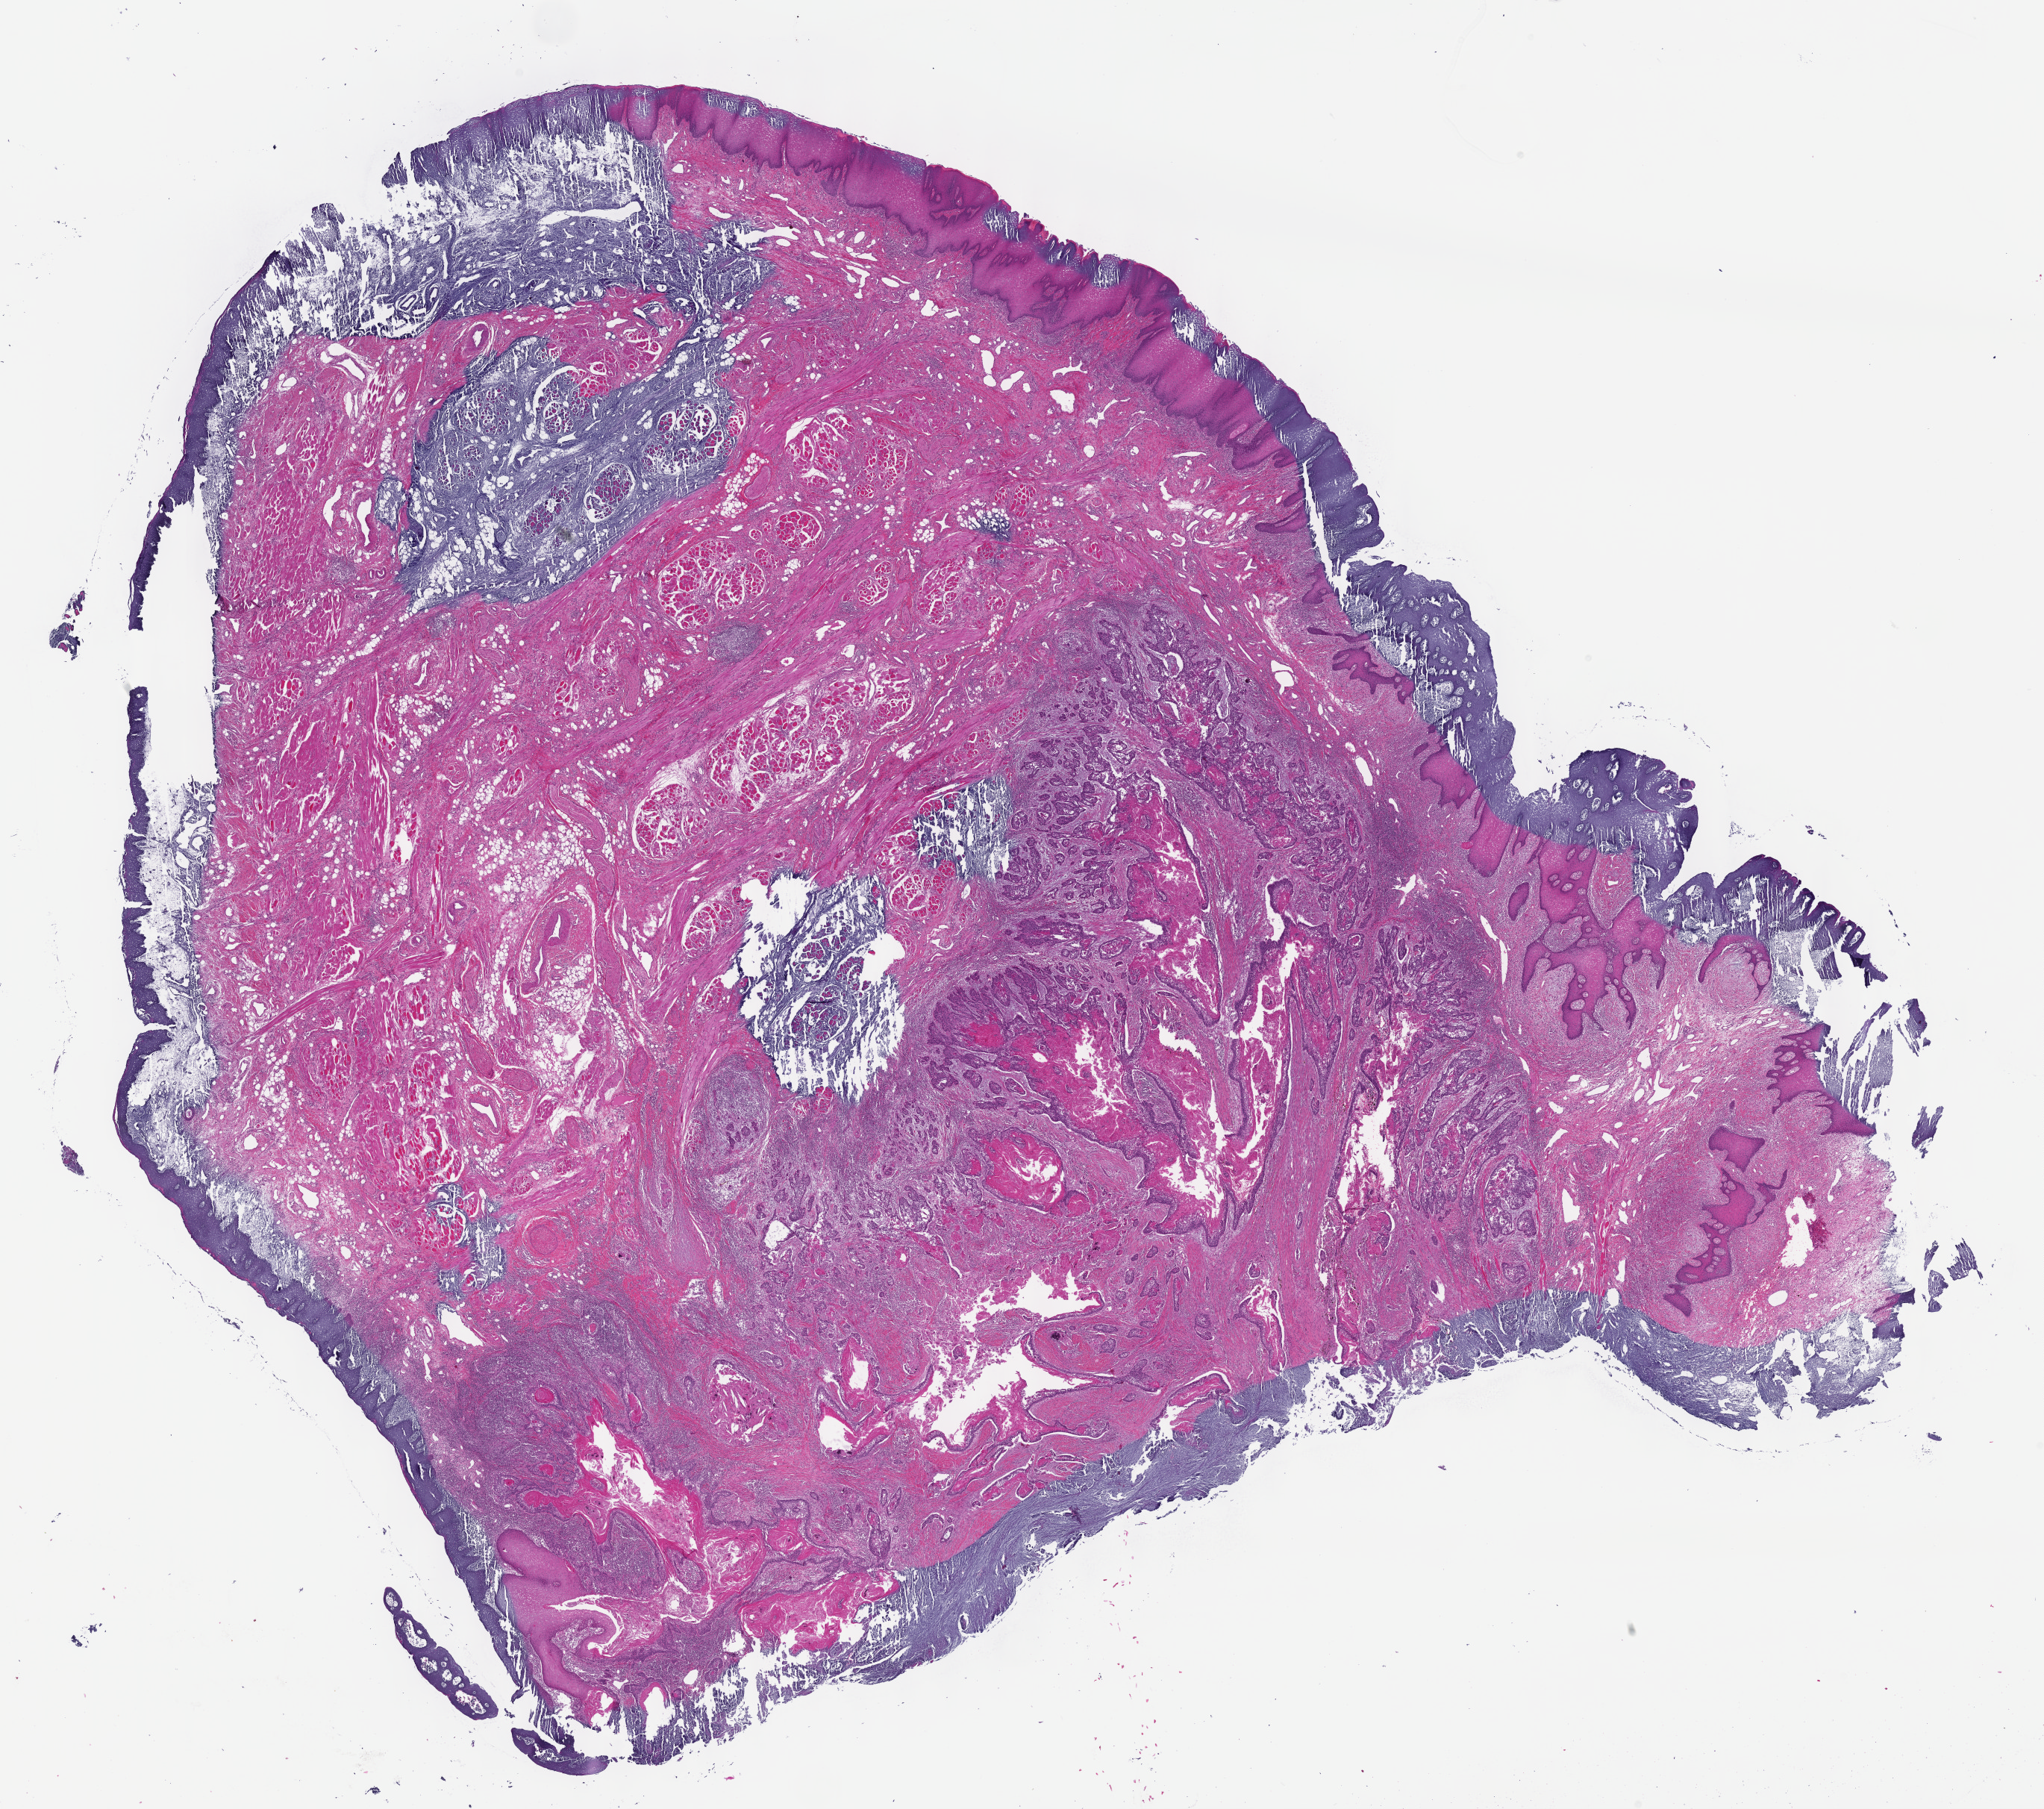
Whole-slide histology image, H&E, shown as a low-resolution overview of the whole scanned area (about 22.1 x 19.6 mm, slide scanned at 40x), formalin-fixed paraffin-embedded (FFPE) diagnostic section, head and neck, primary tumour sample. Male patient; age at initial diagnosis 64 years. Histologic grade: G1 (well differentiated).
Histologic diagnosis: Squamous cell carcinoma, NOS (overlapping lesion of lip, oral cavity and pharynx). AJCC pathologic stage: II.